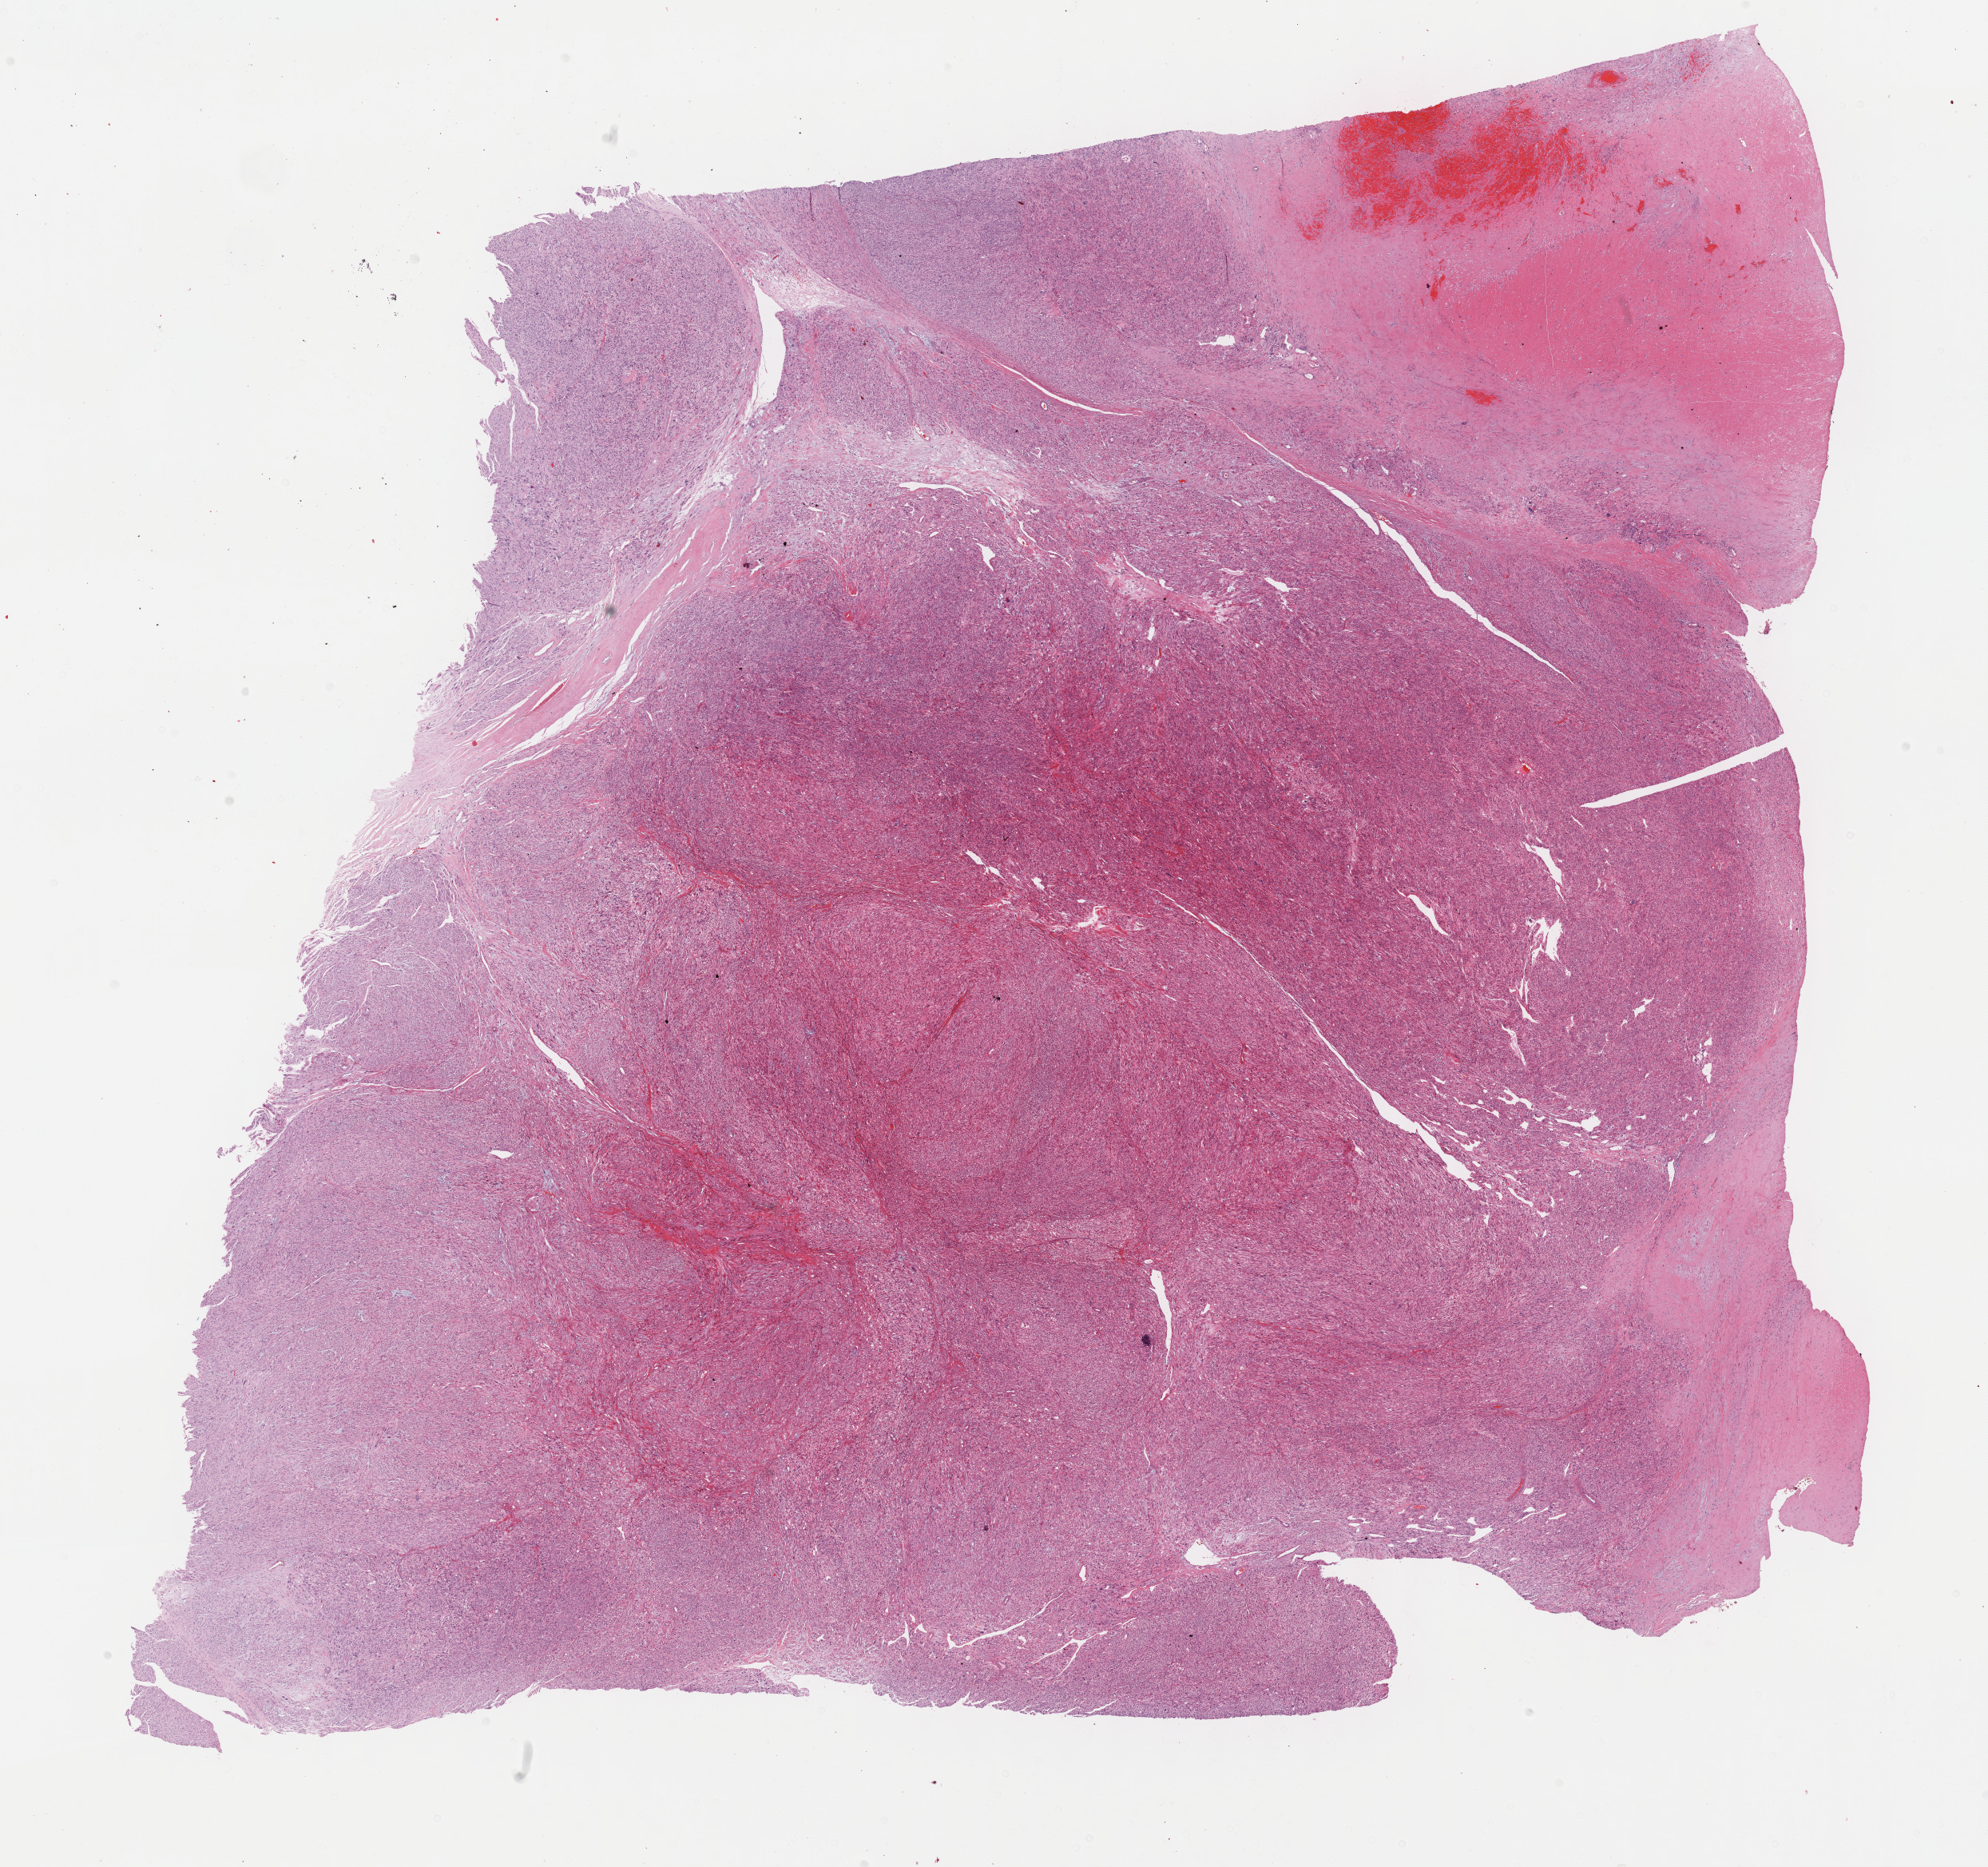
H&E-stained whole-slide image — a low-resolution overview of the entire scanned area, about 20.1 x 18.9 mm (slide scanned at 40x); formalin-fixed paraffin-embedded (FFPE) diagnostic section; sample: primary tumour, connective, subcutaneous and other soft tissues. Female patient; age at initial diagnosis 56 years.
Pathologic diagnosis: Leiomyosarcoma, NOS (connective, subcutaneous and other soft tissues of abdomen).